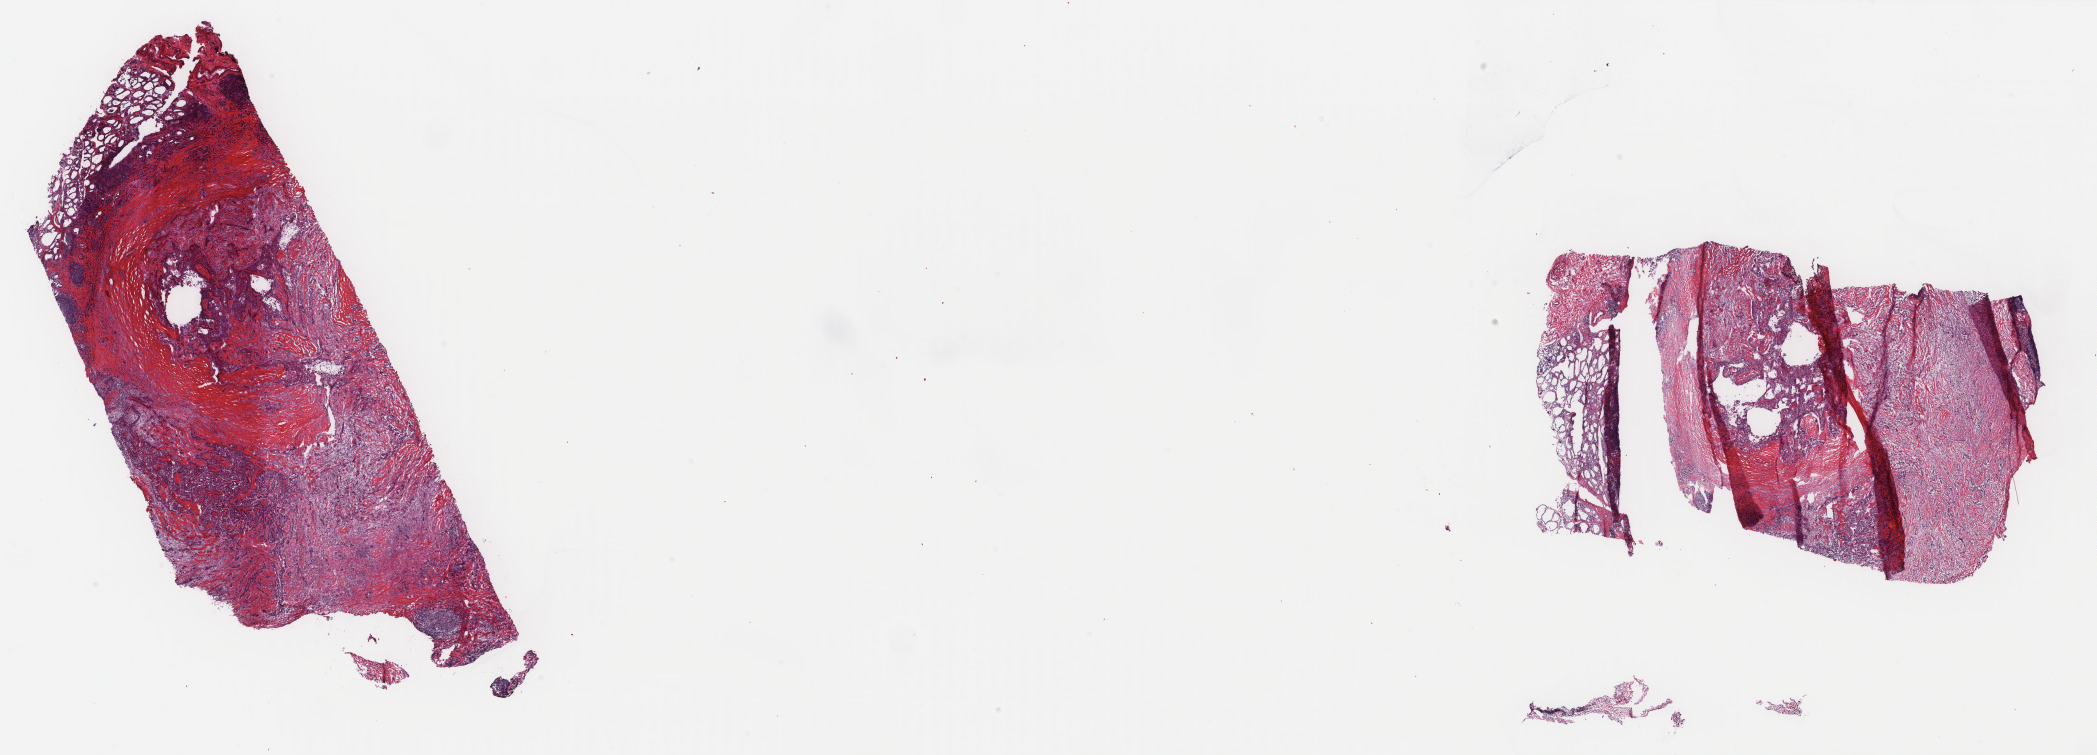
Digitized H&E-stained tissue section (whole slide) — whole scanned area (about 33.3 x 12.0 mm) shown as a low-resolution overview. Frozen section from the top of the tissue portion. Thyroid, primary tumour sample. Patient: female, age at initial diagnosis 65 years. Composition of this section per pathologist review: tumour cells 60%, tumour nuclei 70%, normal cells 10%, stromal cells 30%, necrosis 0%. Infiltration values recorded for this section: lymphocyte infiltration 4%, monocyte infiltration 1%, neutrophil infiltration 0%.
TNM: T1b N1a M0. Laterality: right. AJCC pathologic stage: III (7th edition). Diagnosis: Papillary carcinoma, columnar cell (thyroid gland). Lymph nodes positive (case pathology): 1 of 5 examined.